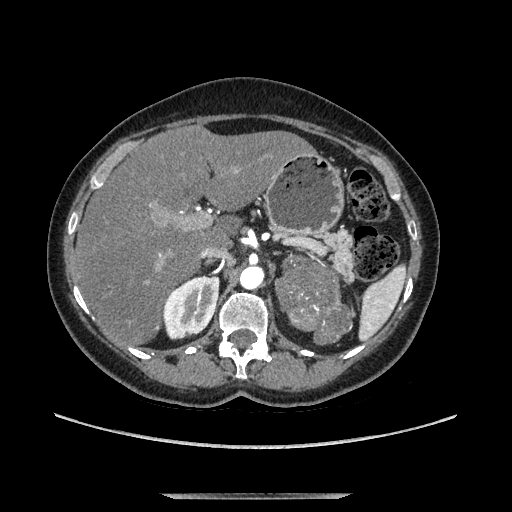
Contrast-enhanced abdominal CT, one axial slice; slice 80 of 169 in the series (ordered by position); soft-tissue window (W 400 / L 40 HU); 512 × 512 image matrix, field of view 400 × 400 mm. Female patient. Case-level facts recorded for this patient, not image findings: diagnosis: adrenocortical carcinoma; tumour side: left adrenal; tumour size at pathology: 9 cm; Ki-67 index: 2 %; stage (as recorded): 3.
Annotated regions visible in this slice (semi-automatic segmentation, software-assisted and operator-edited):
- mass: box from (x=279, y=255) to (x=349, y=341) px